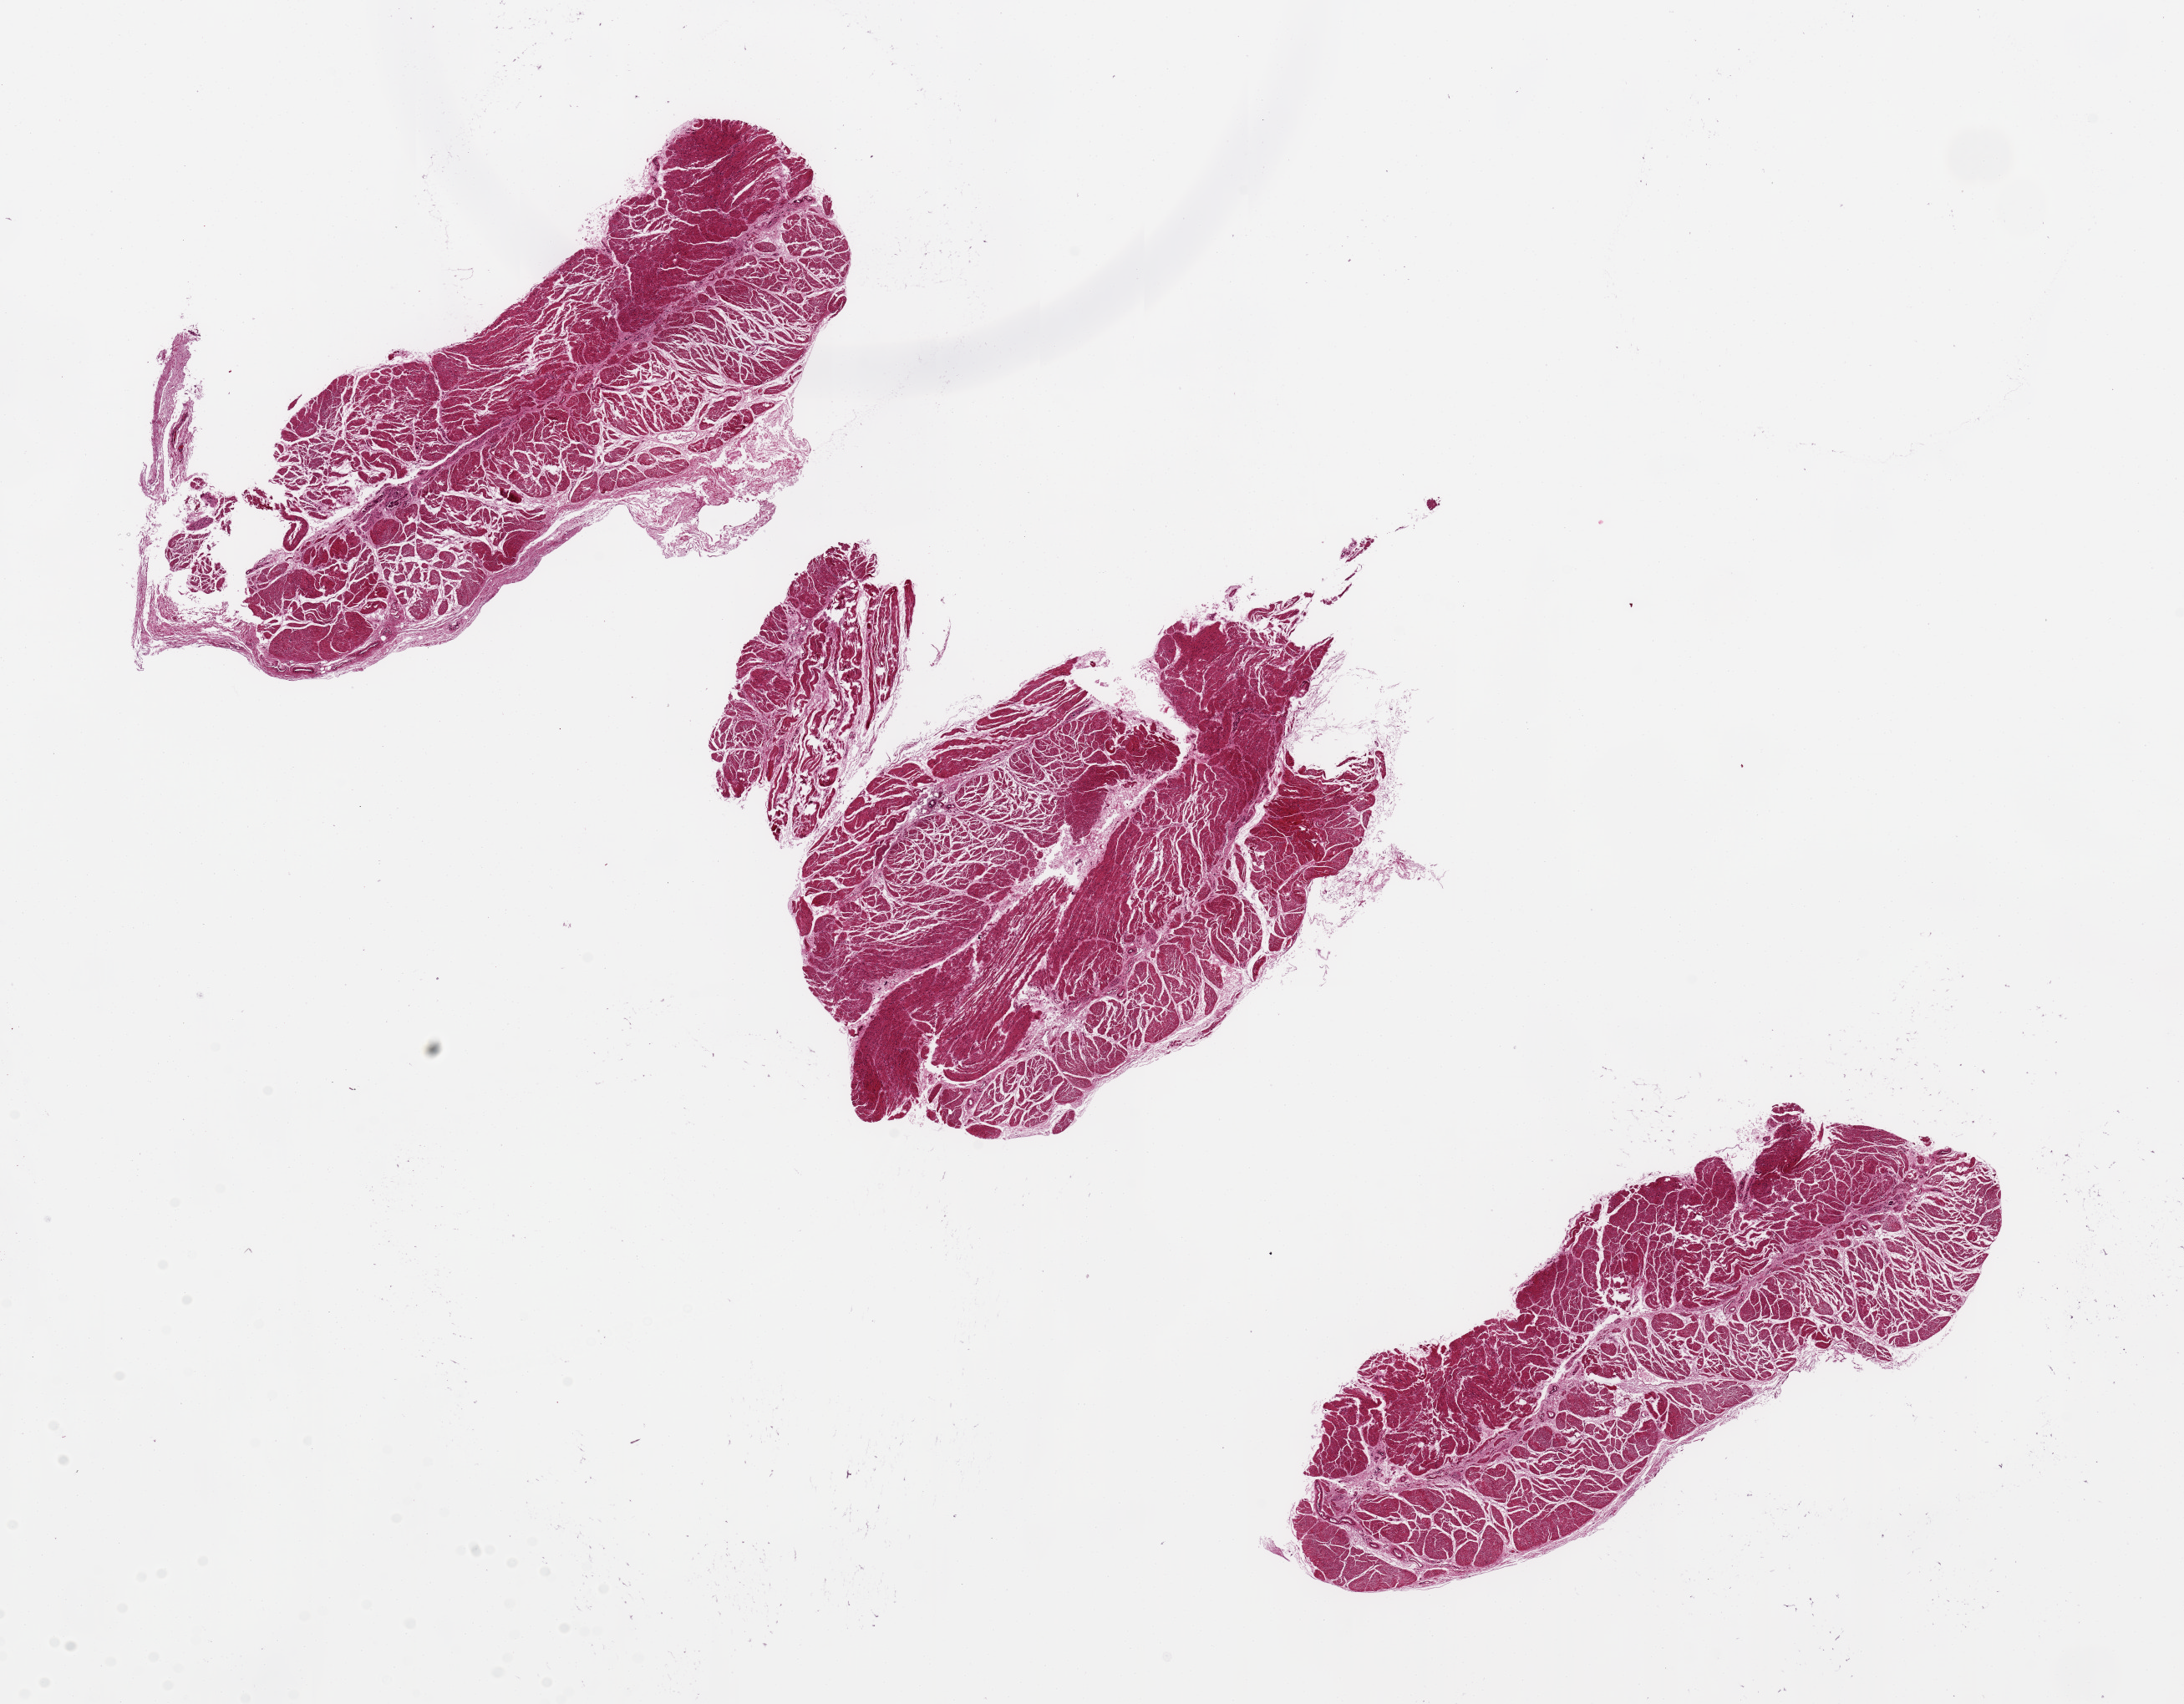
Haematoxylin and eosin whole-slide image, shown as a low-resolution overview of the whole scanned area (about 20.7 x 16.1 mm, acquisition: 20x scan). PAXgene-fixed paraffin-embedded (PFPE) section. Target tissue: esophageal muscle. Tissue donor sample. Male donor.
Pathologist's review note for this sample: 3 ~ 6.5x2.5mm pieces. Poorly fixed.